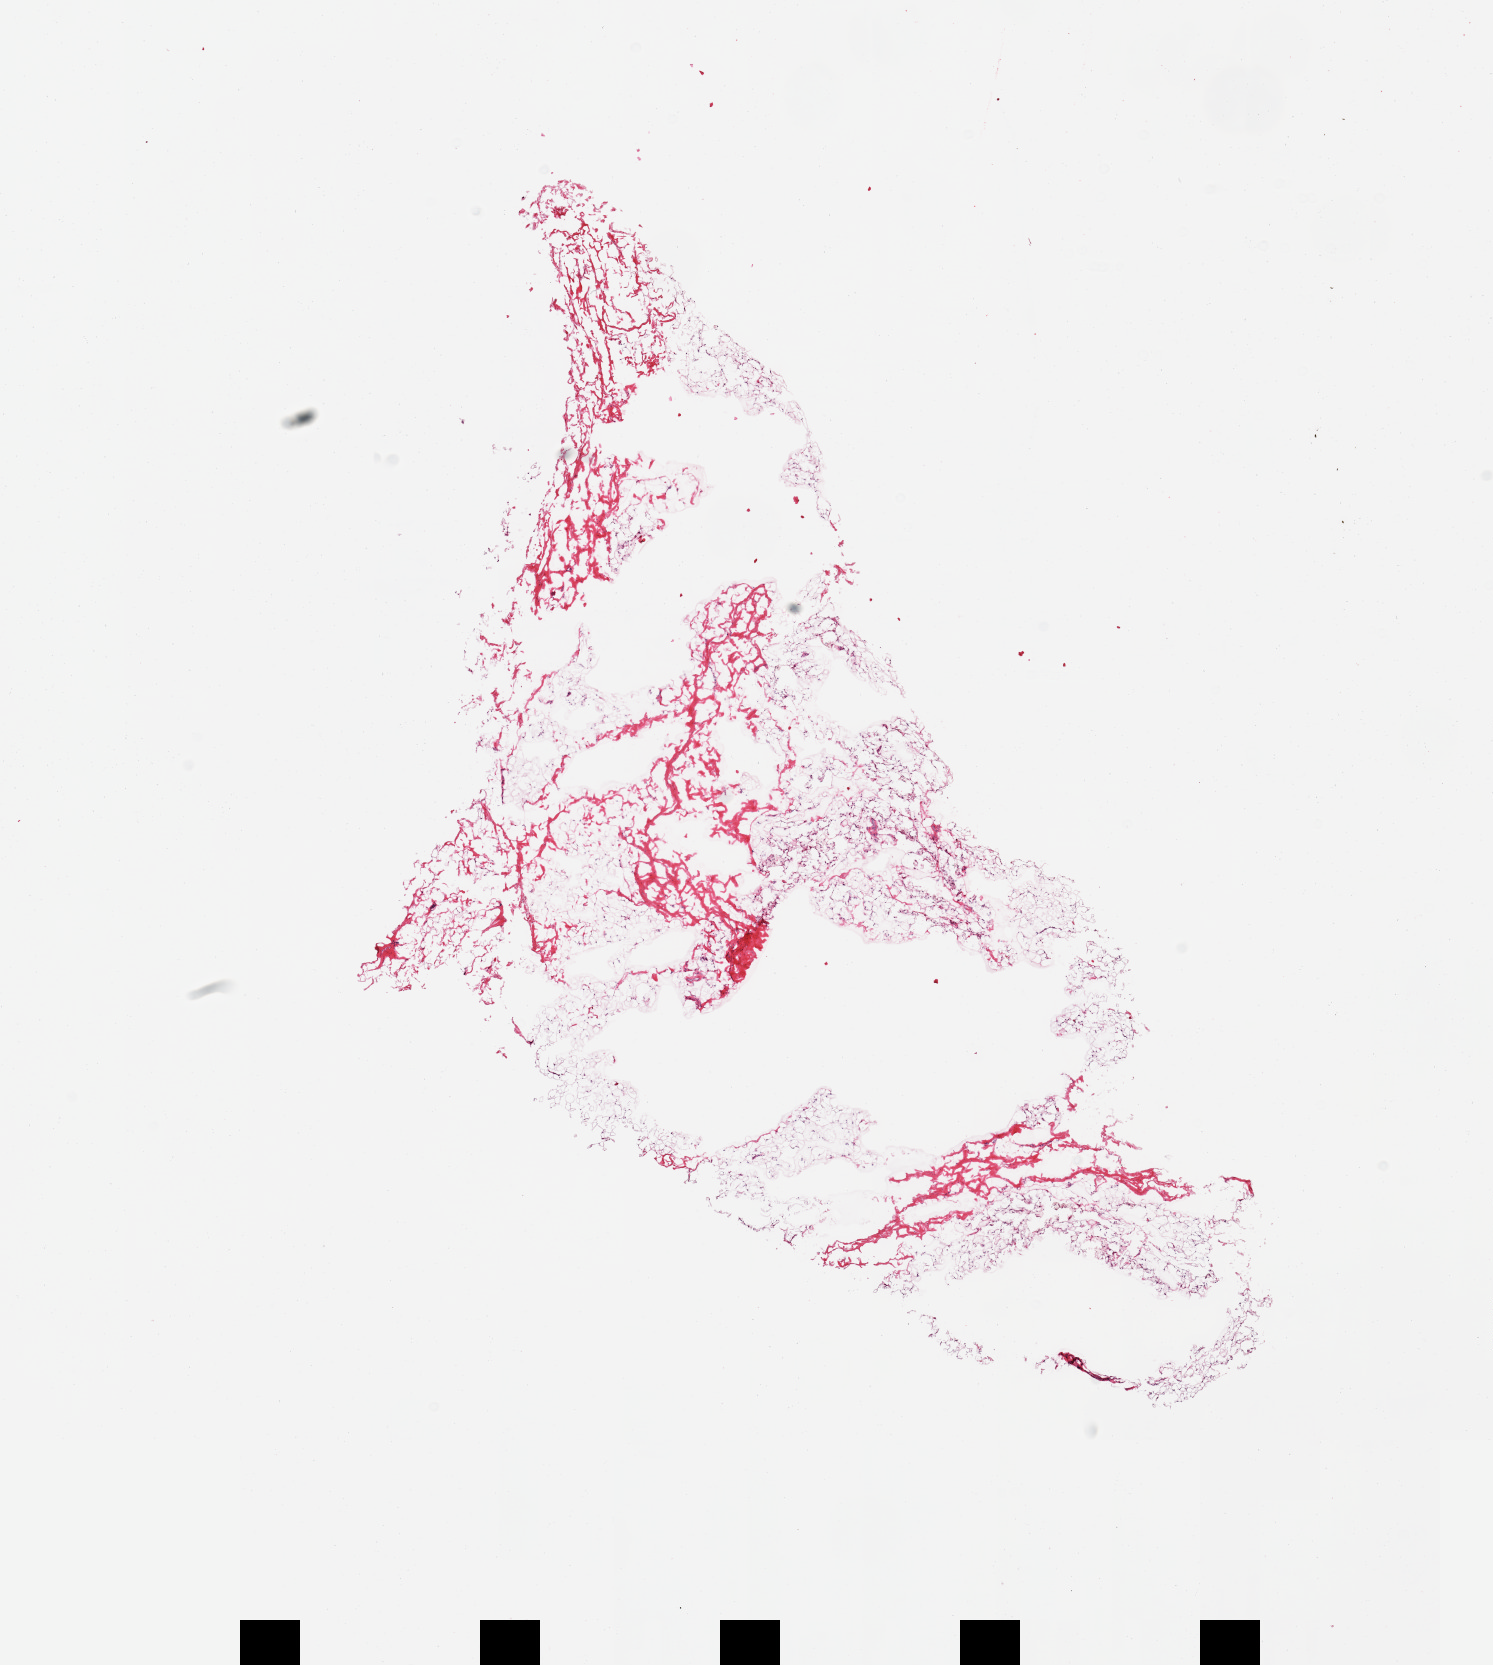
Whole-slide image, hematoxylin and eosin (H&E) stain, shown as a low-resolution overview of the whole scanned area (about 11.8 x 13.2 mm); frozen section; sampled site (target tissue): breast; tissue donor sample. Female donor.
- review note (as recorded): 1 piece; multiple central defects, predominantly fat/fibrous tissue